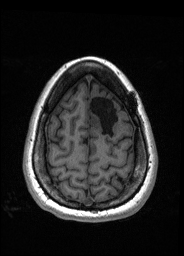
Pre-operative brain MRI before brain-tumour surgery, one axial slice; position 44 of 176 along the scan axis; T1-weighted post-contrast; 1 mm slice thickness; 184 × 256 image matrix, field of view 180 × 250 mm. Case-level facts recorded for this patient, not image findings: histopathology: Oligodendroglioma; WHO grade: 2; IDH mutation: yes.
Structures marked on this image (expert manual segmentation):
- tumour: bounding box <89,113,101,126> (left, top, right, bottom; pixels)